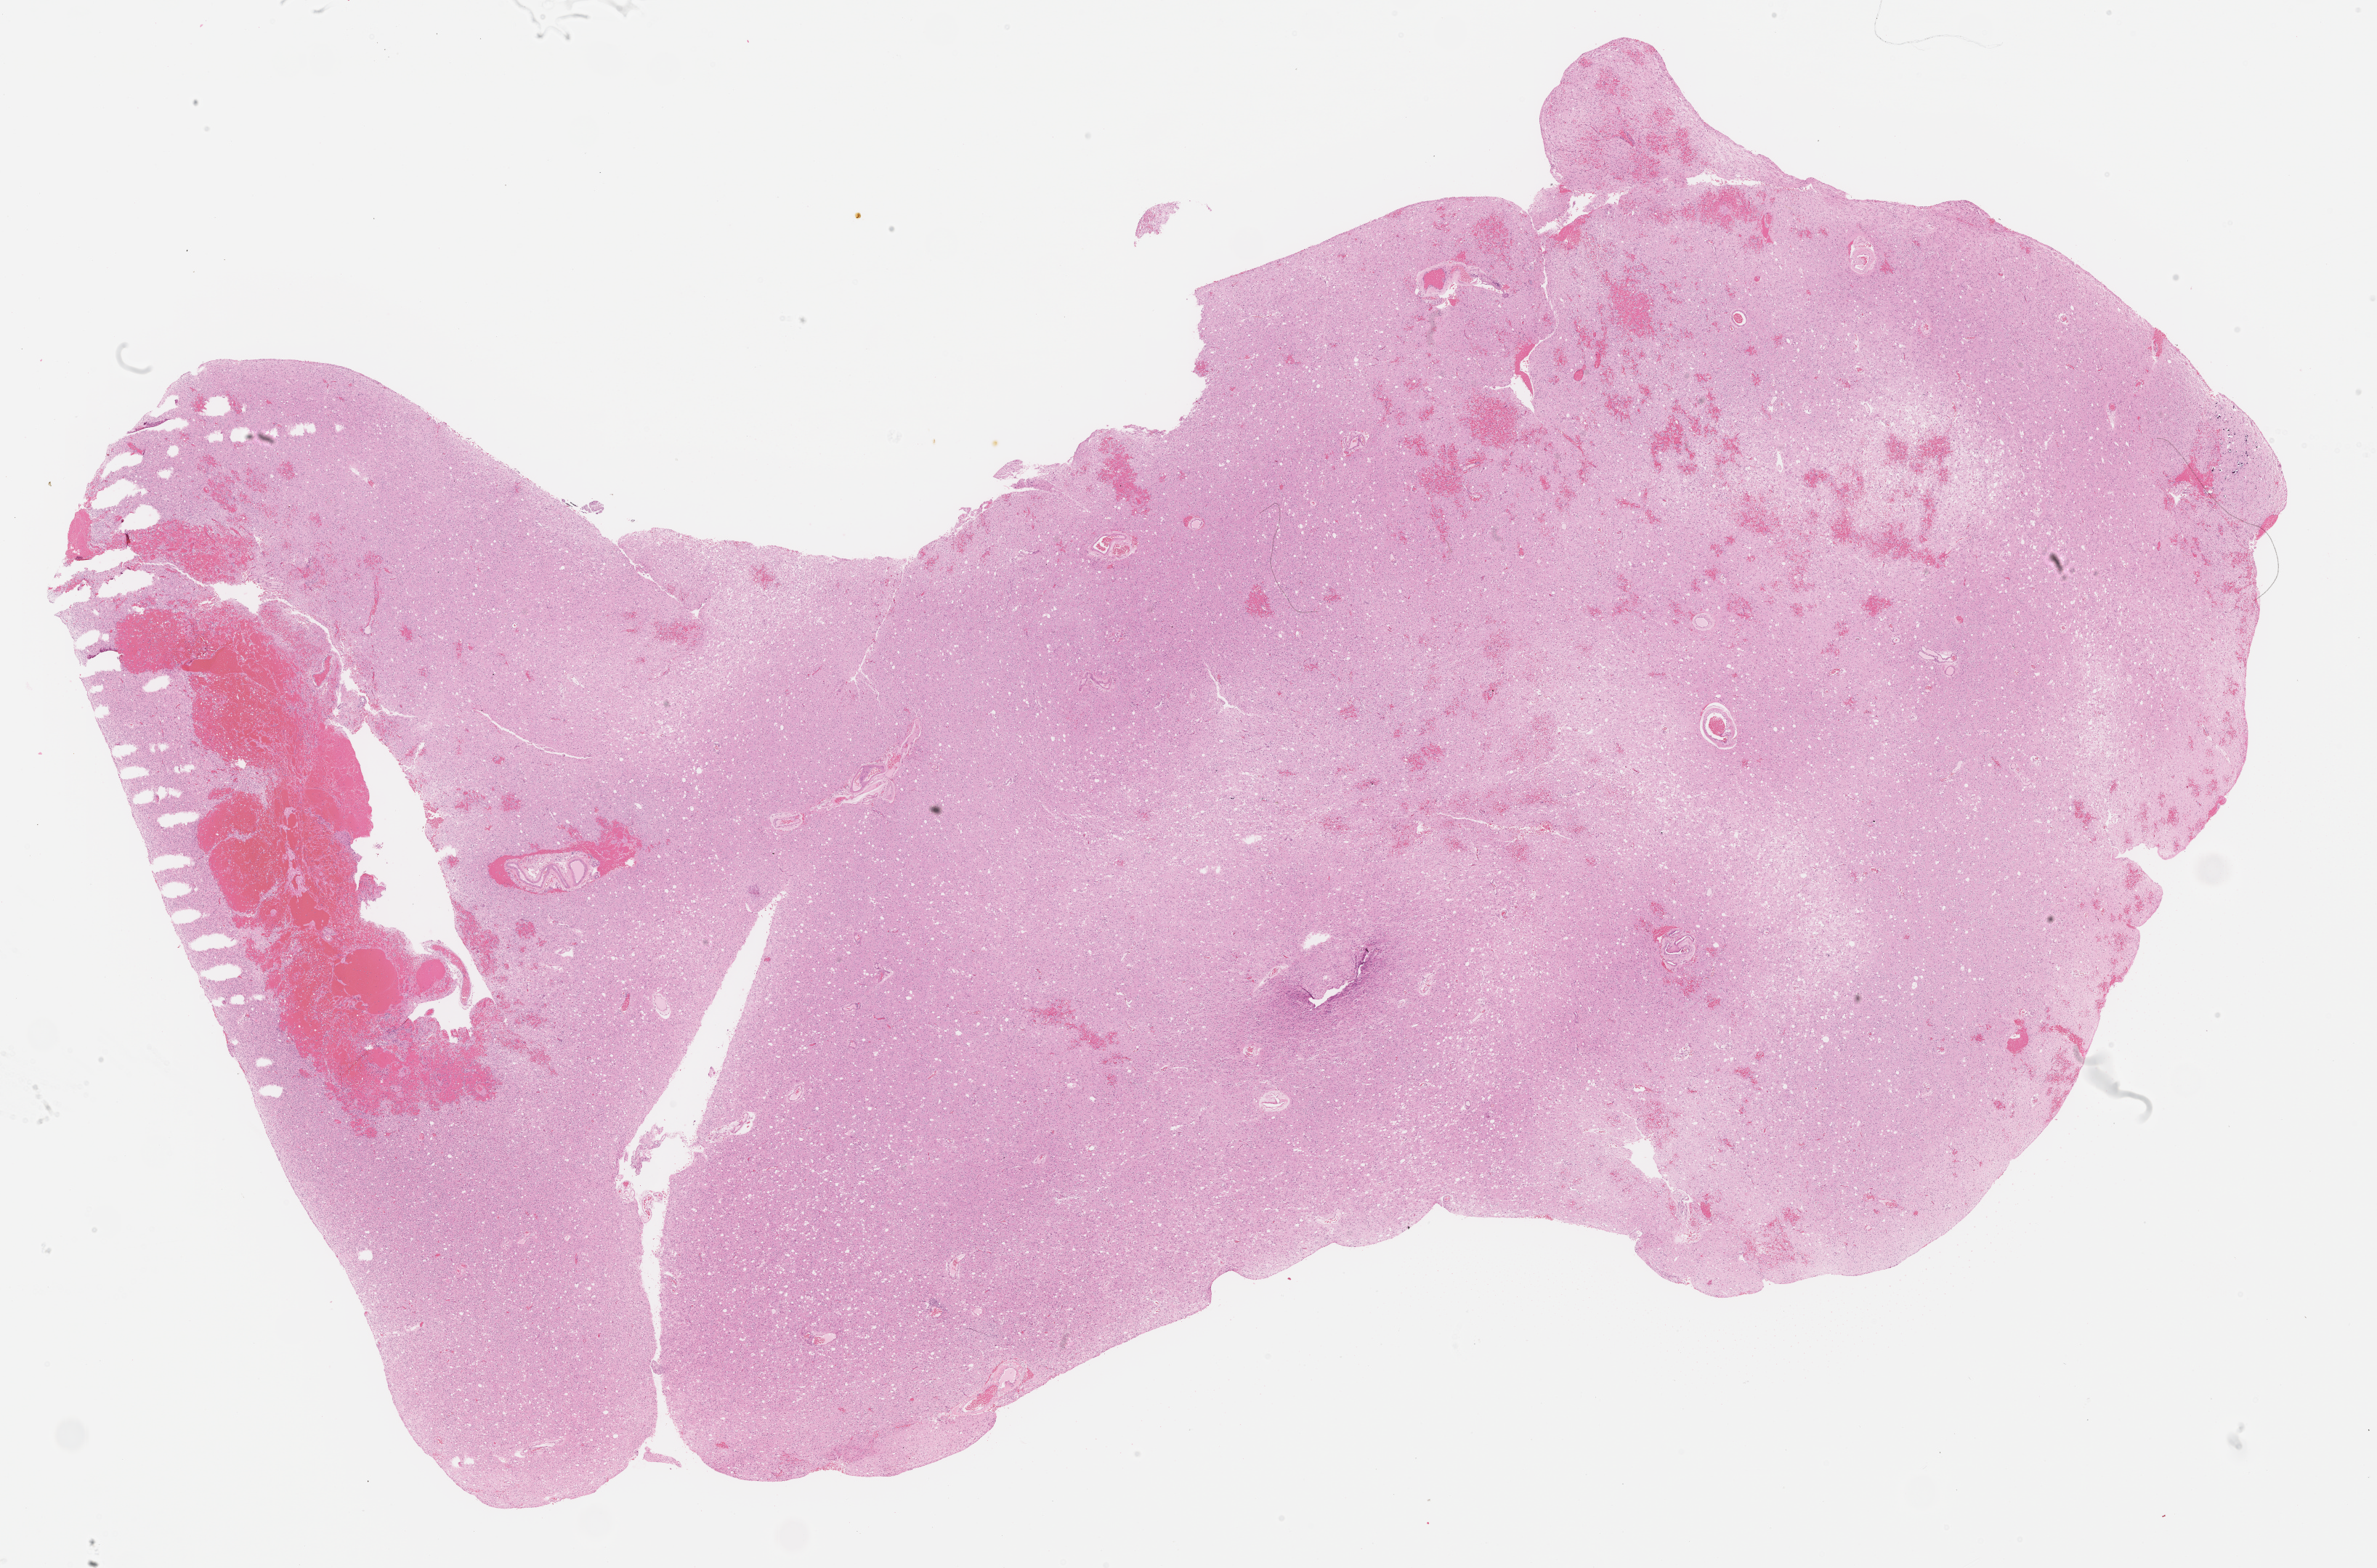
Hematoxylin and eosin (H&E) stained whole-slide image — whole scanned area (about 26.4 x 17.4 mm, from a 40x scan) shown as a low-resolution overview, FFPE section, sample: primary tumour, brain. Patient: male, age at initial diagnosis 52 years. Histologic grade: G3 (poorly differentiated).
* pathologic diagnosis: Oligodendroglioma, anaplastic (cerebrum)
* laterality: left